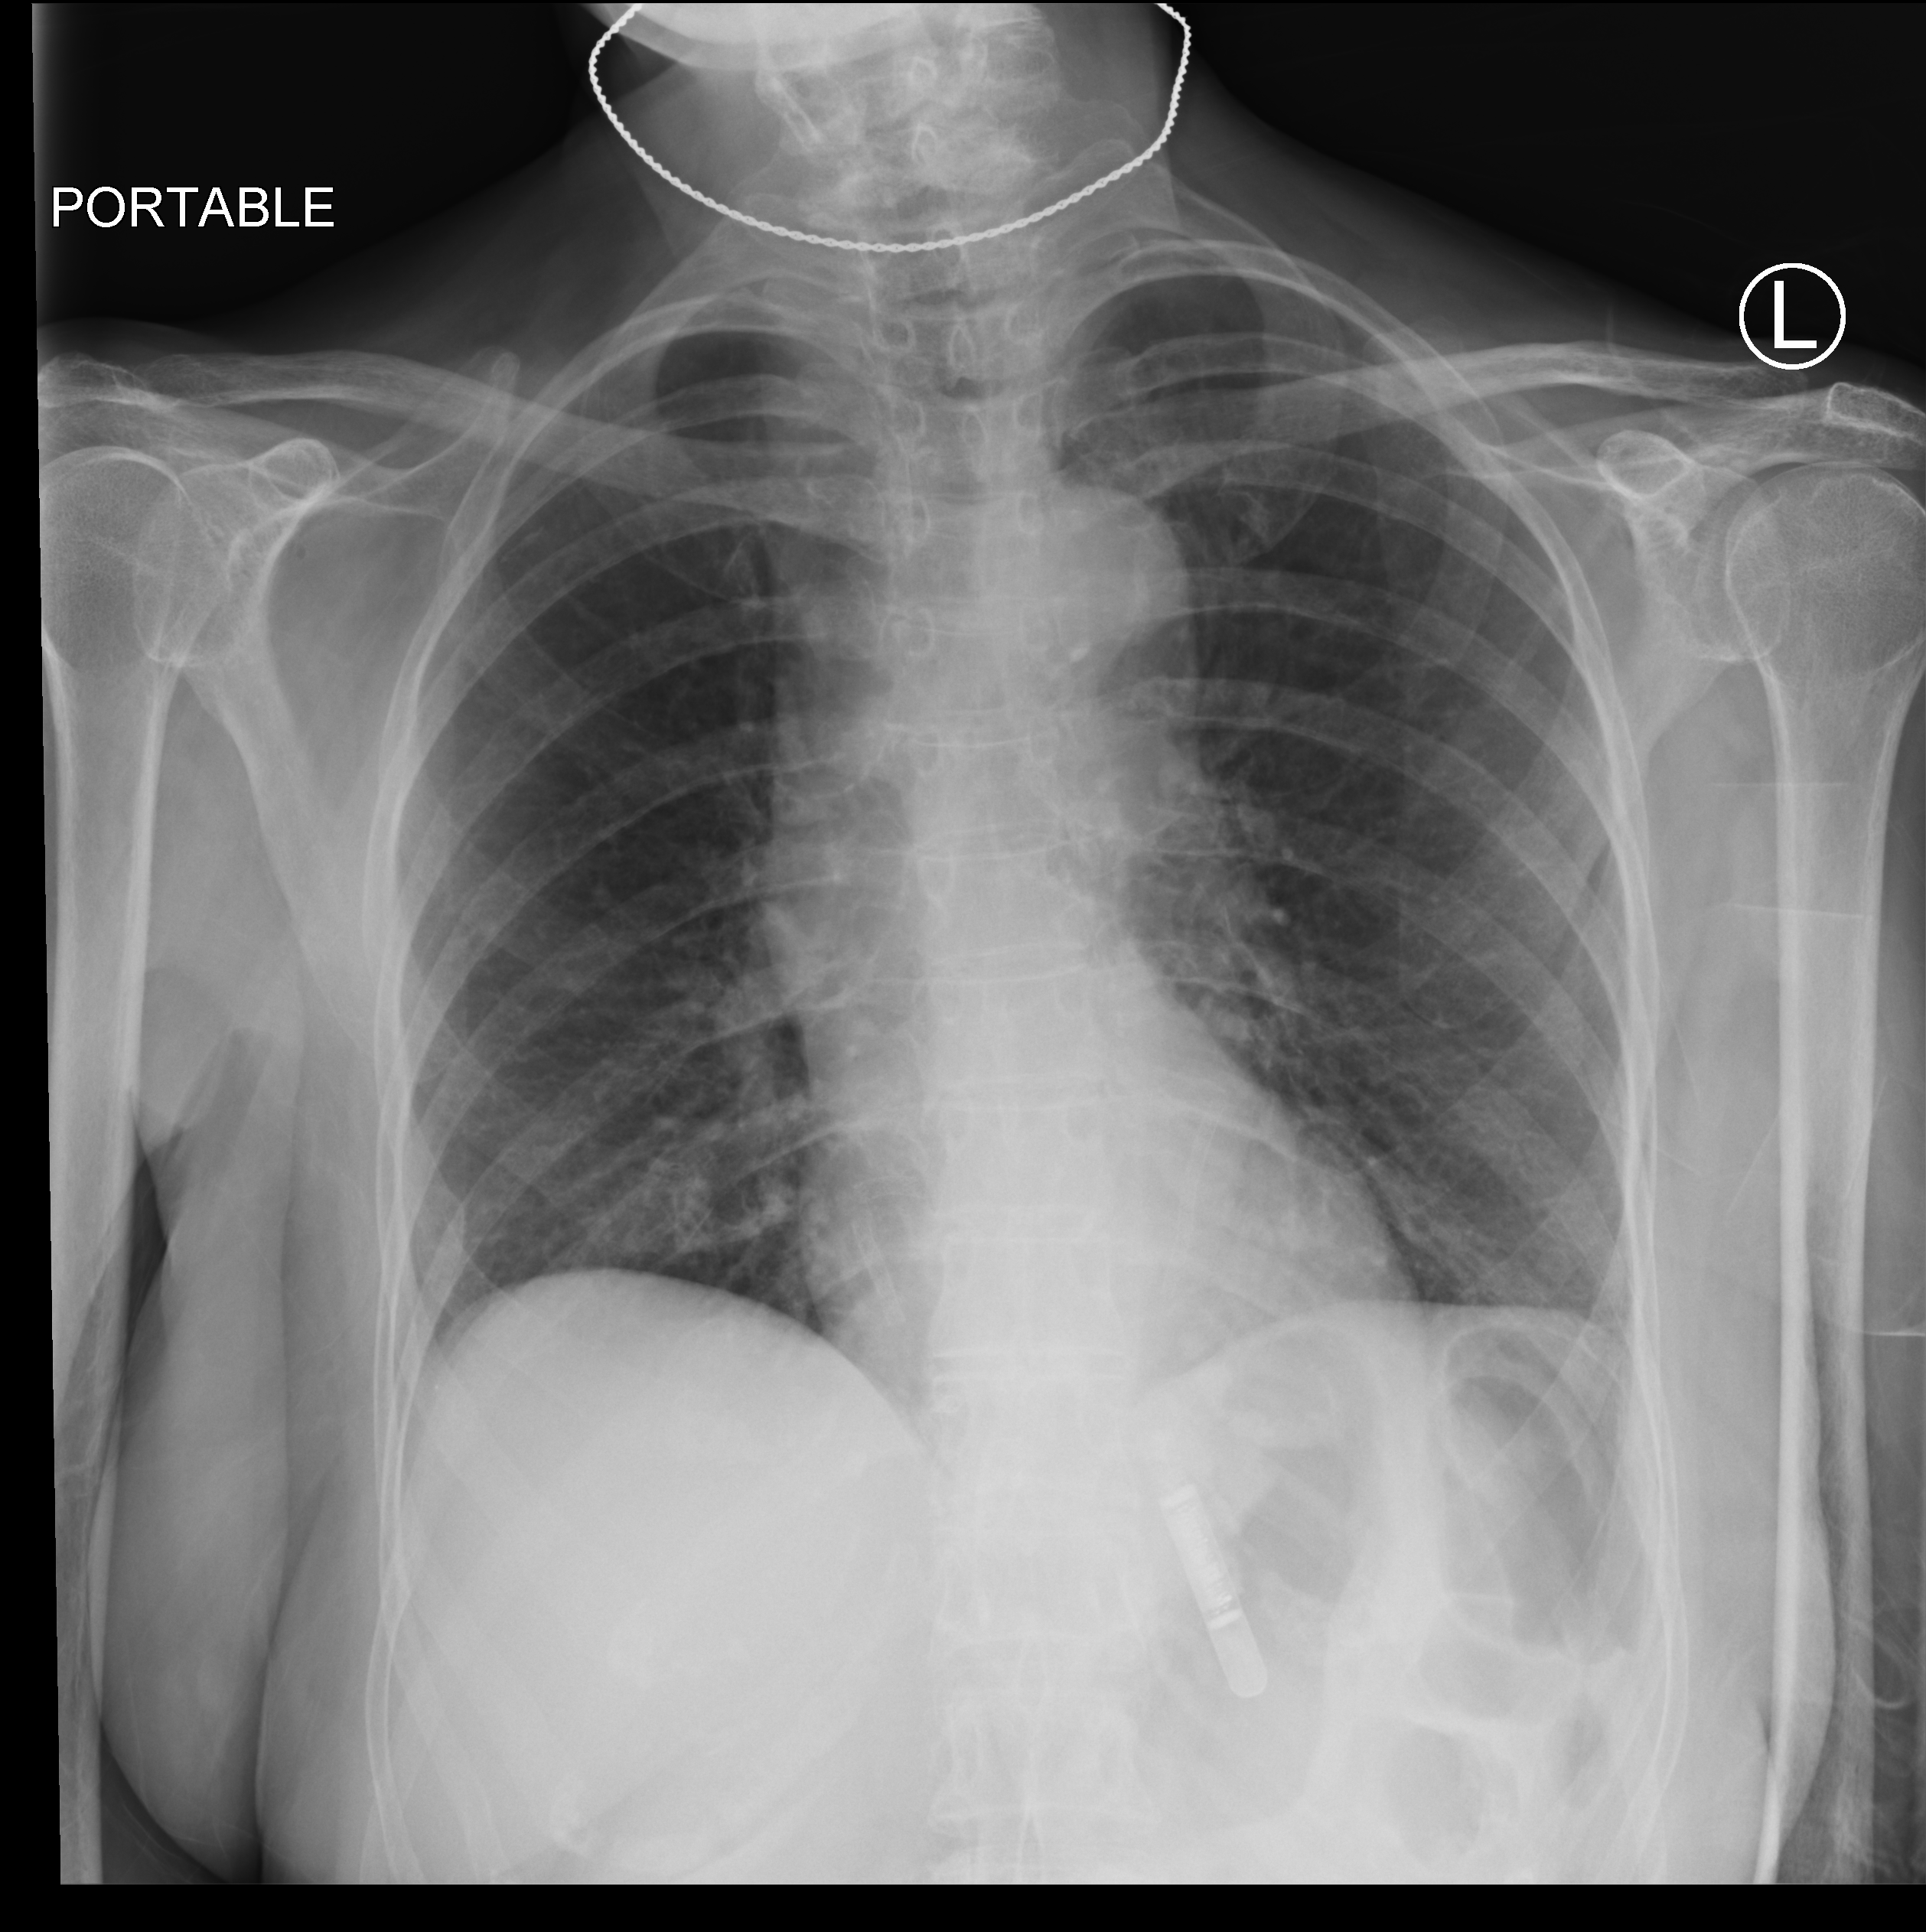
Portable chest radiograph, anteroposterior (AP) projection. Patient hospitalised with COVID-19; female, aged 60–74 years.
From the hospital-stay record, not from the radiograph (when in the stay this image was taken is not recorded): smoking status (admission record): never; mechanically ventilated during this hospital stay: no; admitted to intensive care during this hospital stay: no.